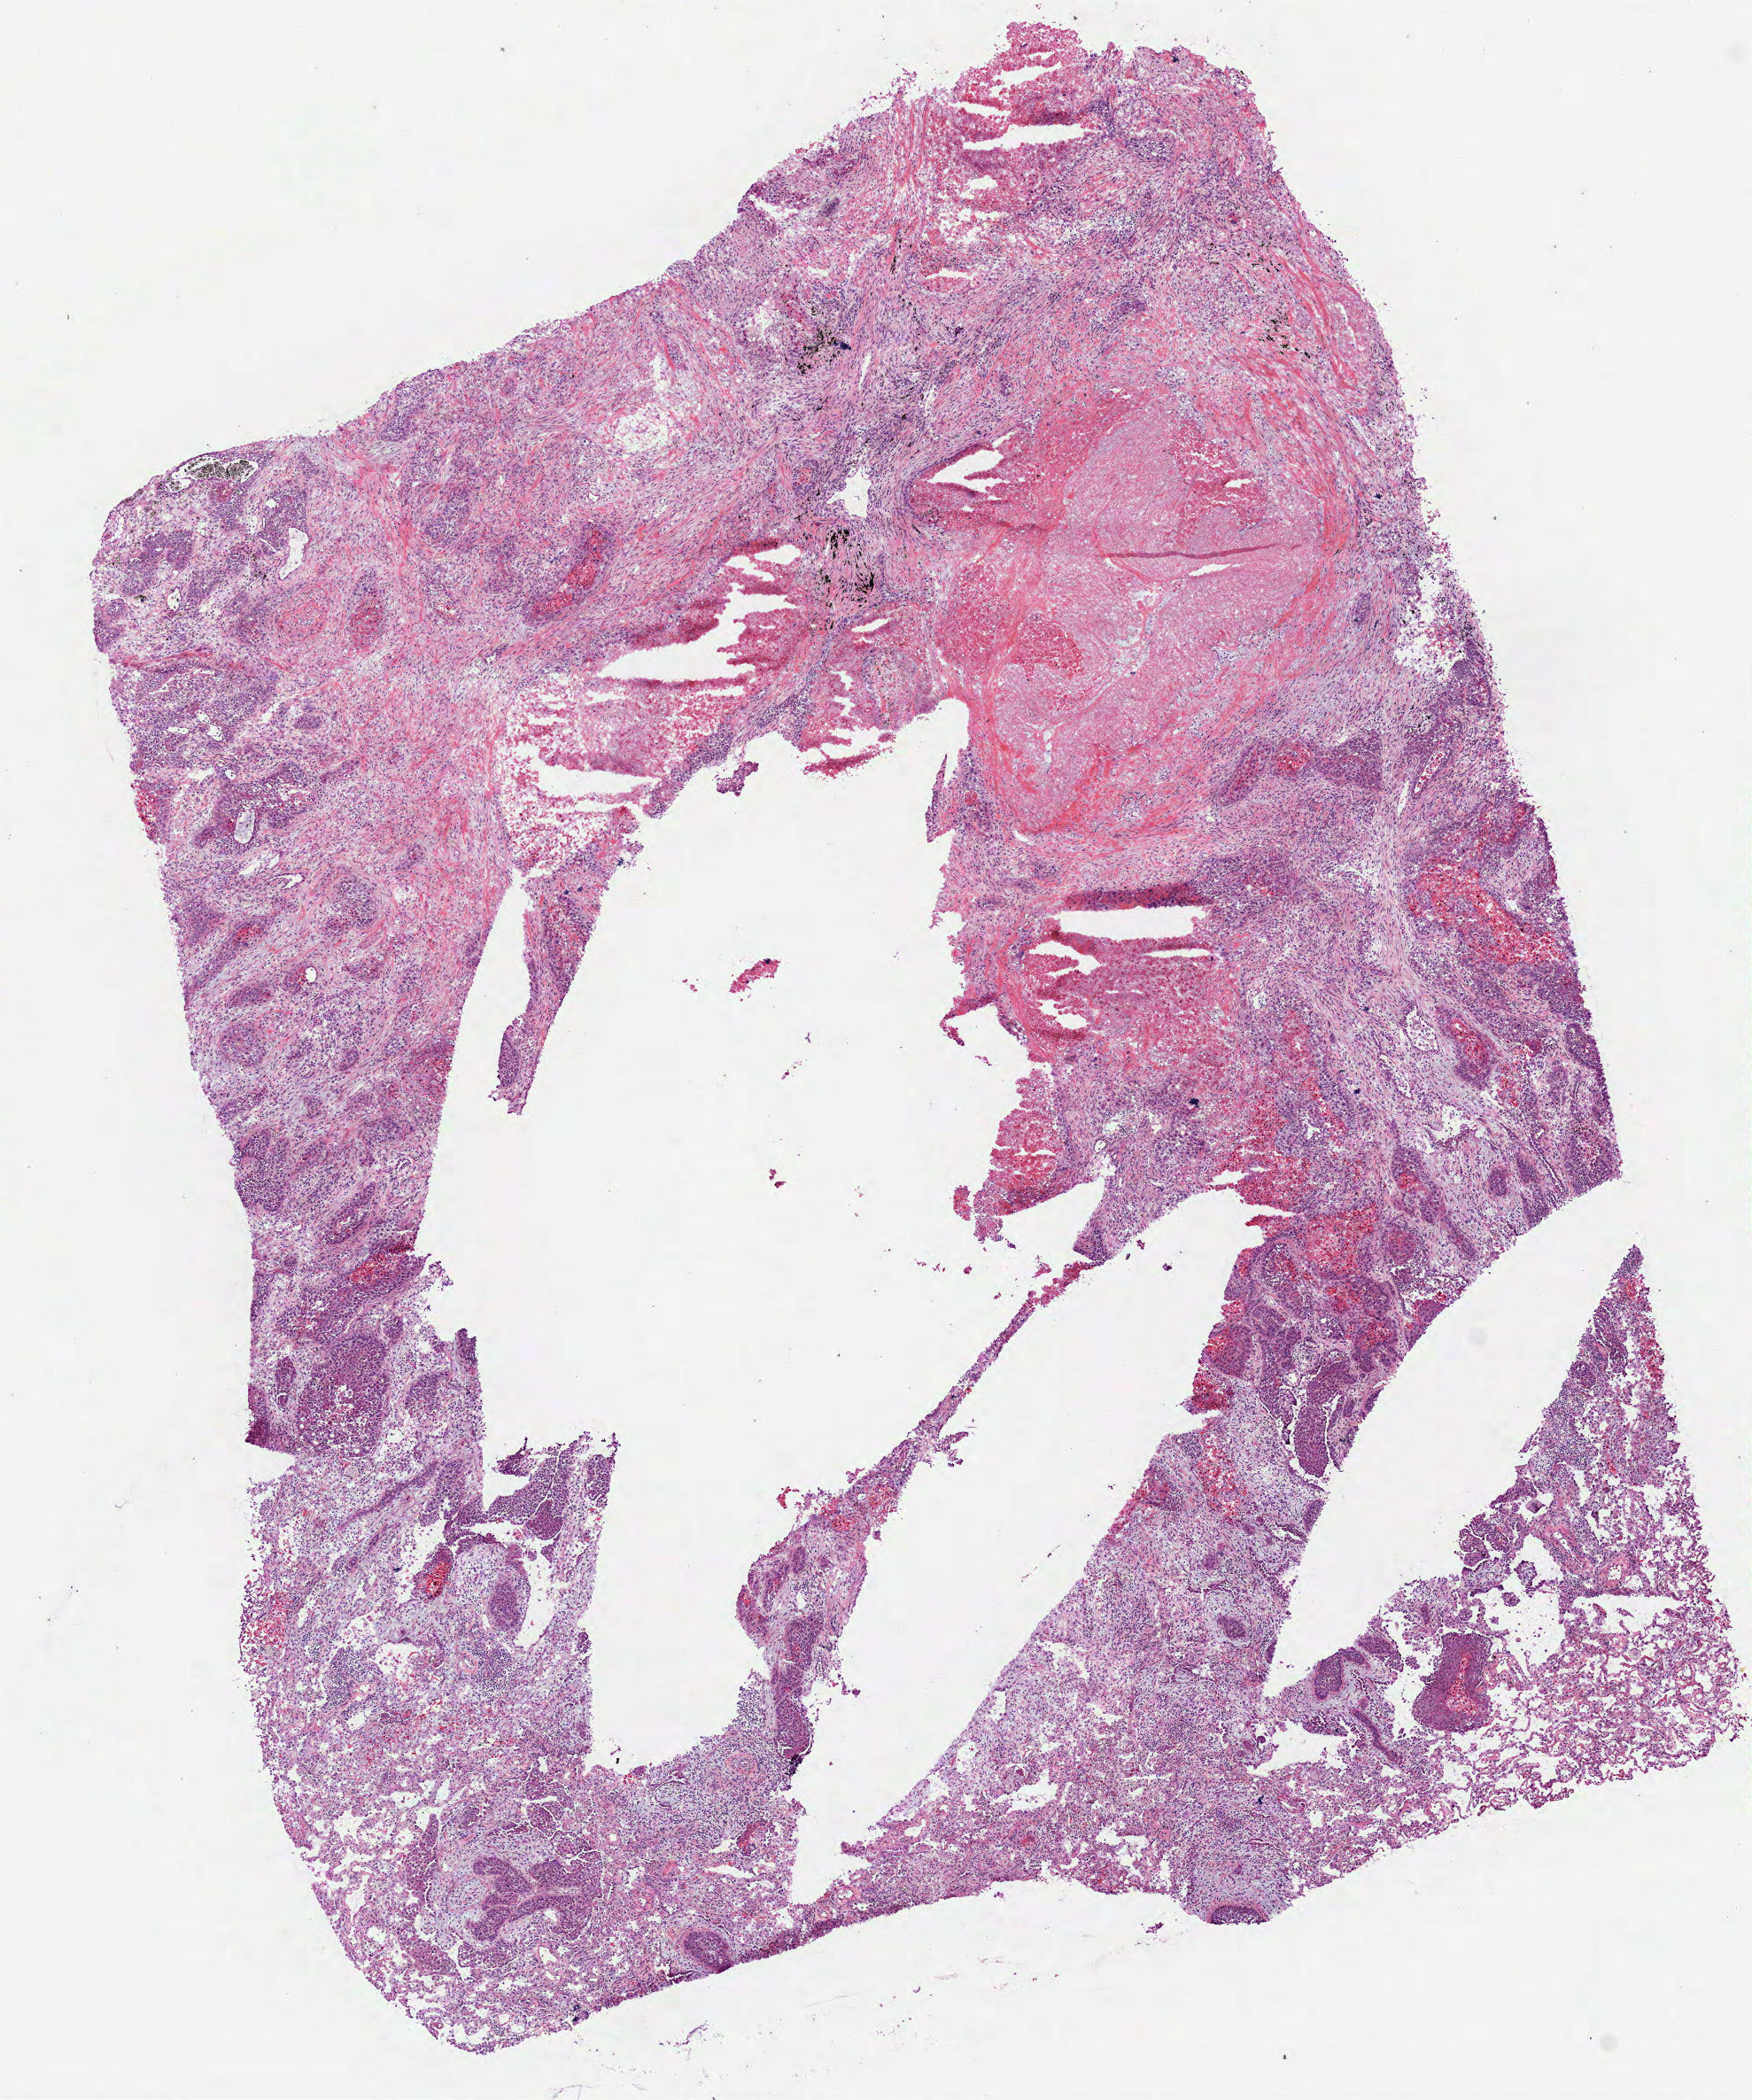
Digitized Hematoxylin and eosin (H&E) stained tissue section (whole slide), low-resolution overview of the scanned area, about 8.0 x 9.6 mm. Frozen section from the bottom of the tissue portion. Lung, primary tumour sample. Male patient; age at initial diagnosis 84 years. Slide review estimates, as recorded: tumour cells 50%, tumour nuclei 45%.
Diagnosis: Squamous cell carcinoma, NOS (upper lobe, lung).